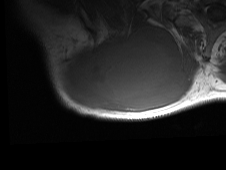
MRI of an extremity soft-tissue mass, one axial slice; position 49 of 81 along the scan axis; MR volume resampled by the dataset authors to the PET/CT grid (not the native acquisition matrix); 3.27 mm slice thickness; 226 × 170 image matrix. Male patient. From the clinical record (not read from this slice): histological type: pleiomorphic spindle cell undifferentiated; grade: high; site of the primary tumour: right parascapusular.
Structures marked on this image (expert contour drawn on MRI and transferred to this co-registered scan by the dataset authors):
- gross tumour volume including surrounding oedema: bounding box <57,24,196,116> (left, top, right, bottom; pixels)
- gross tumour volume (mass): <60,26,186,112>